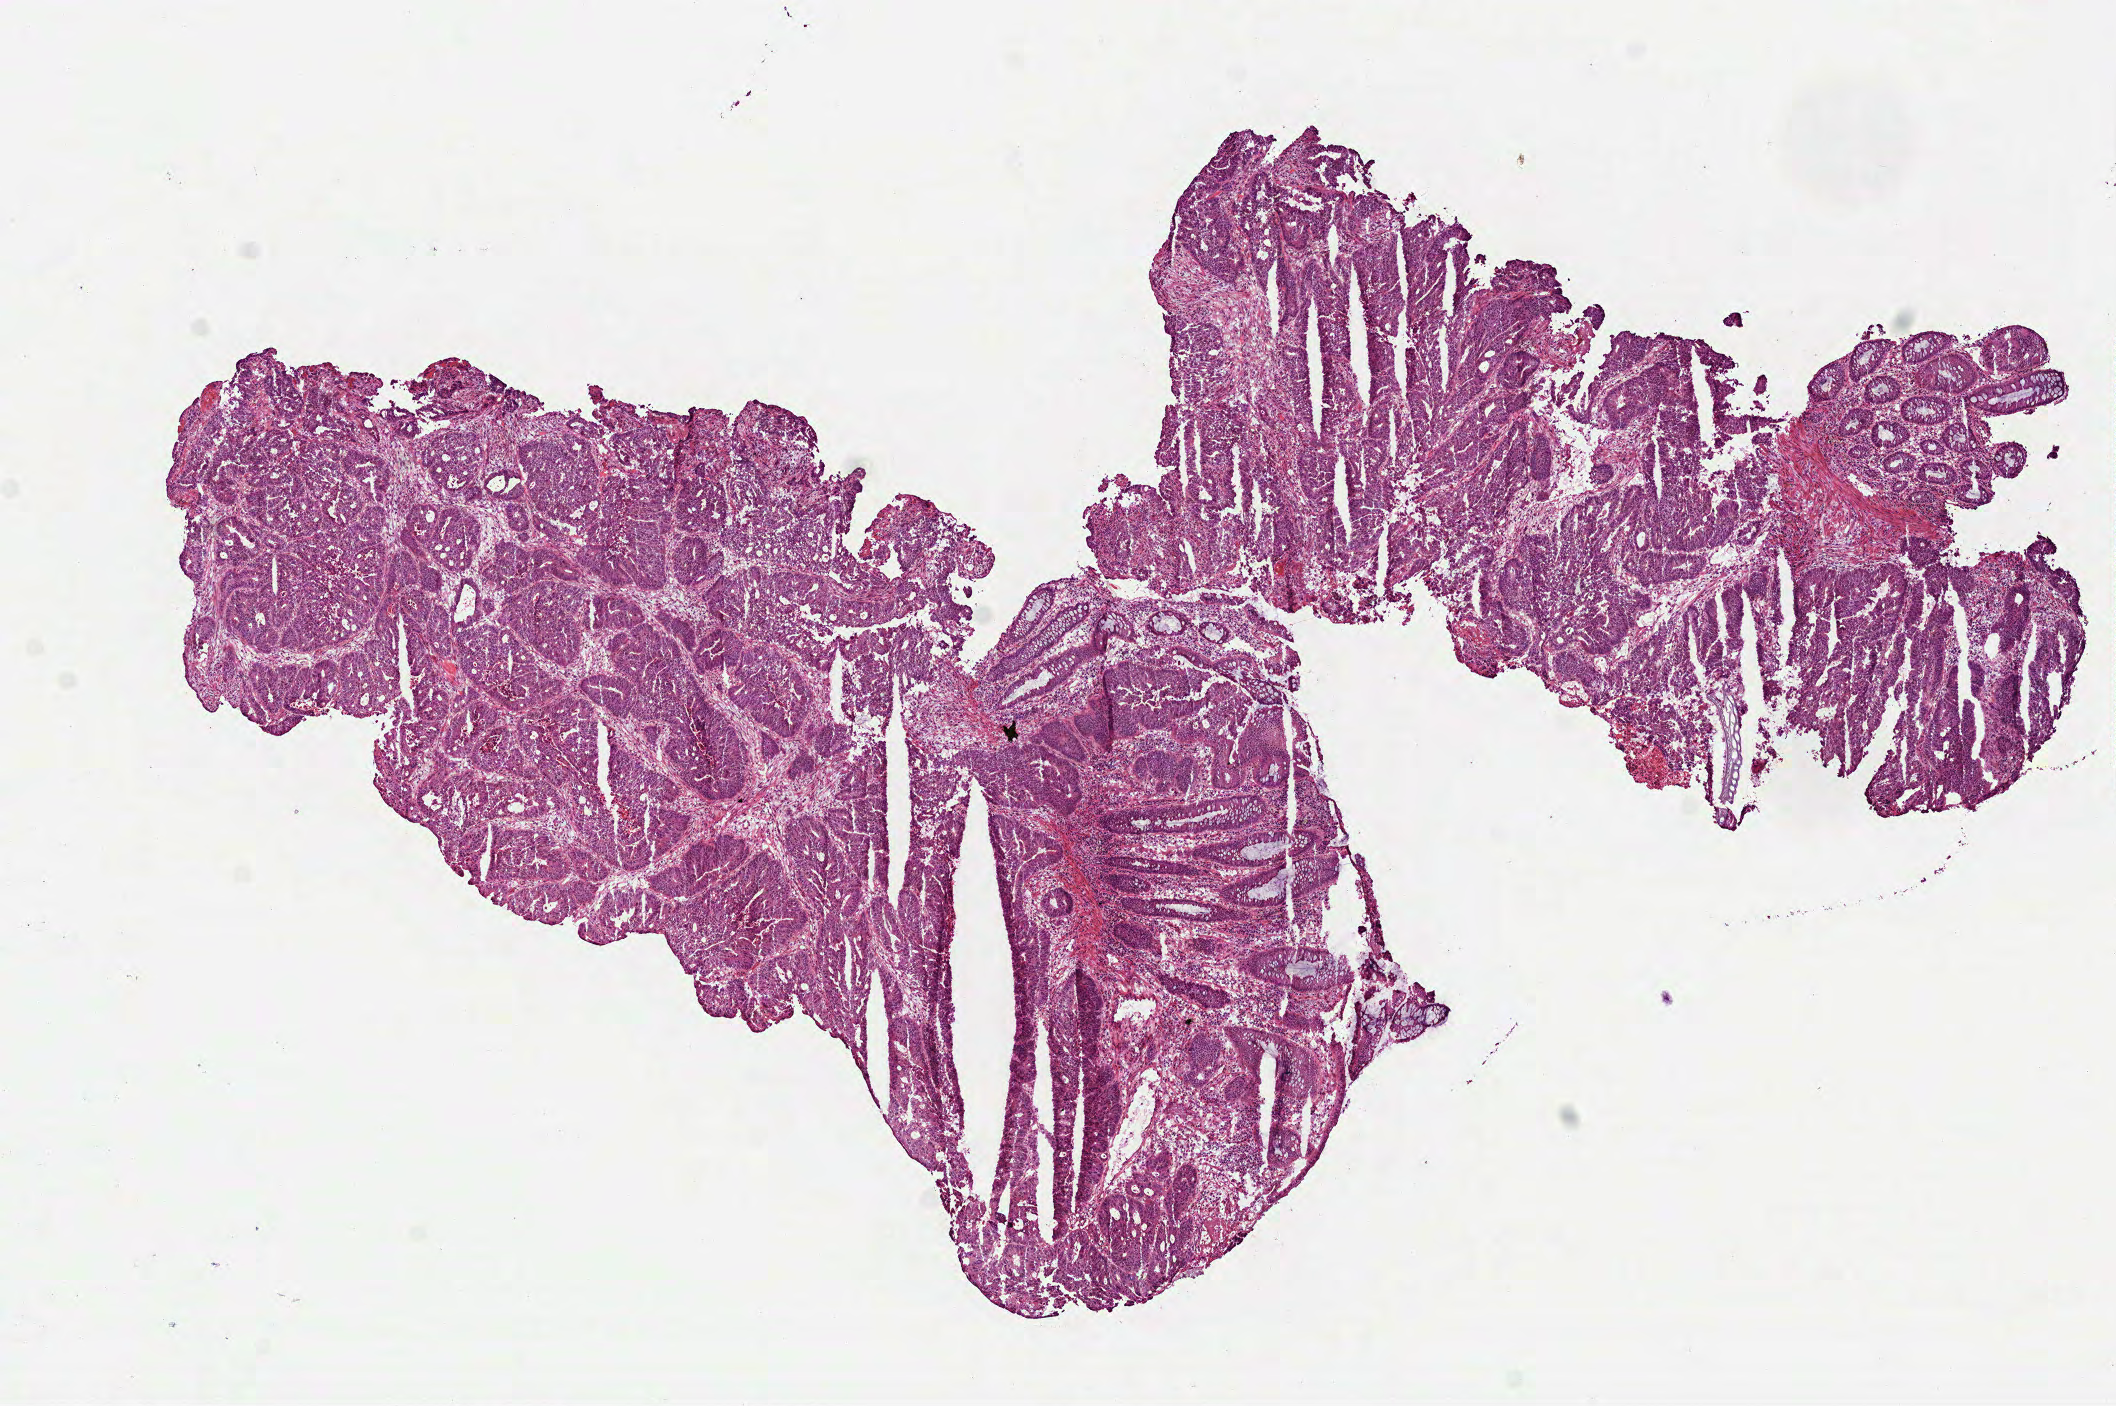
Whole-slide histology image, Hematoxylin and eosin (H&E) stained, whole scanned area (about 8.5 x 5.7 mm) shown as a low-resolution overview. Frozen section from the top of the tissue portion. Primary tumour sample from the rectum. Male patient; age at initial diagnosis 74 years. Slide review estimates, as recorded: tumour cells 75%, tumour nuclei 75%, normal cells 5%, stromal cells 15%, necrosis 5%.
• TNM: T4 N0 M0
• AJCC pathologic stage: IIB (7th edition)
• diagnosis: Adenocarcinoma, NOS